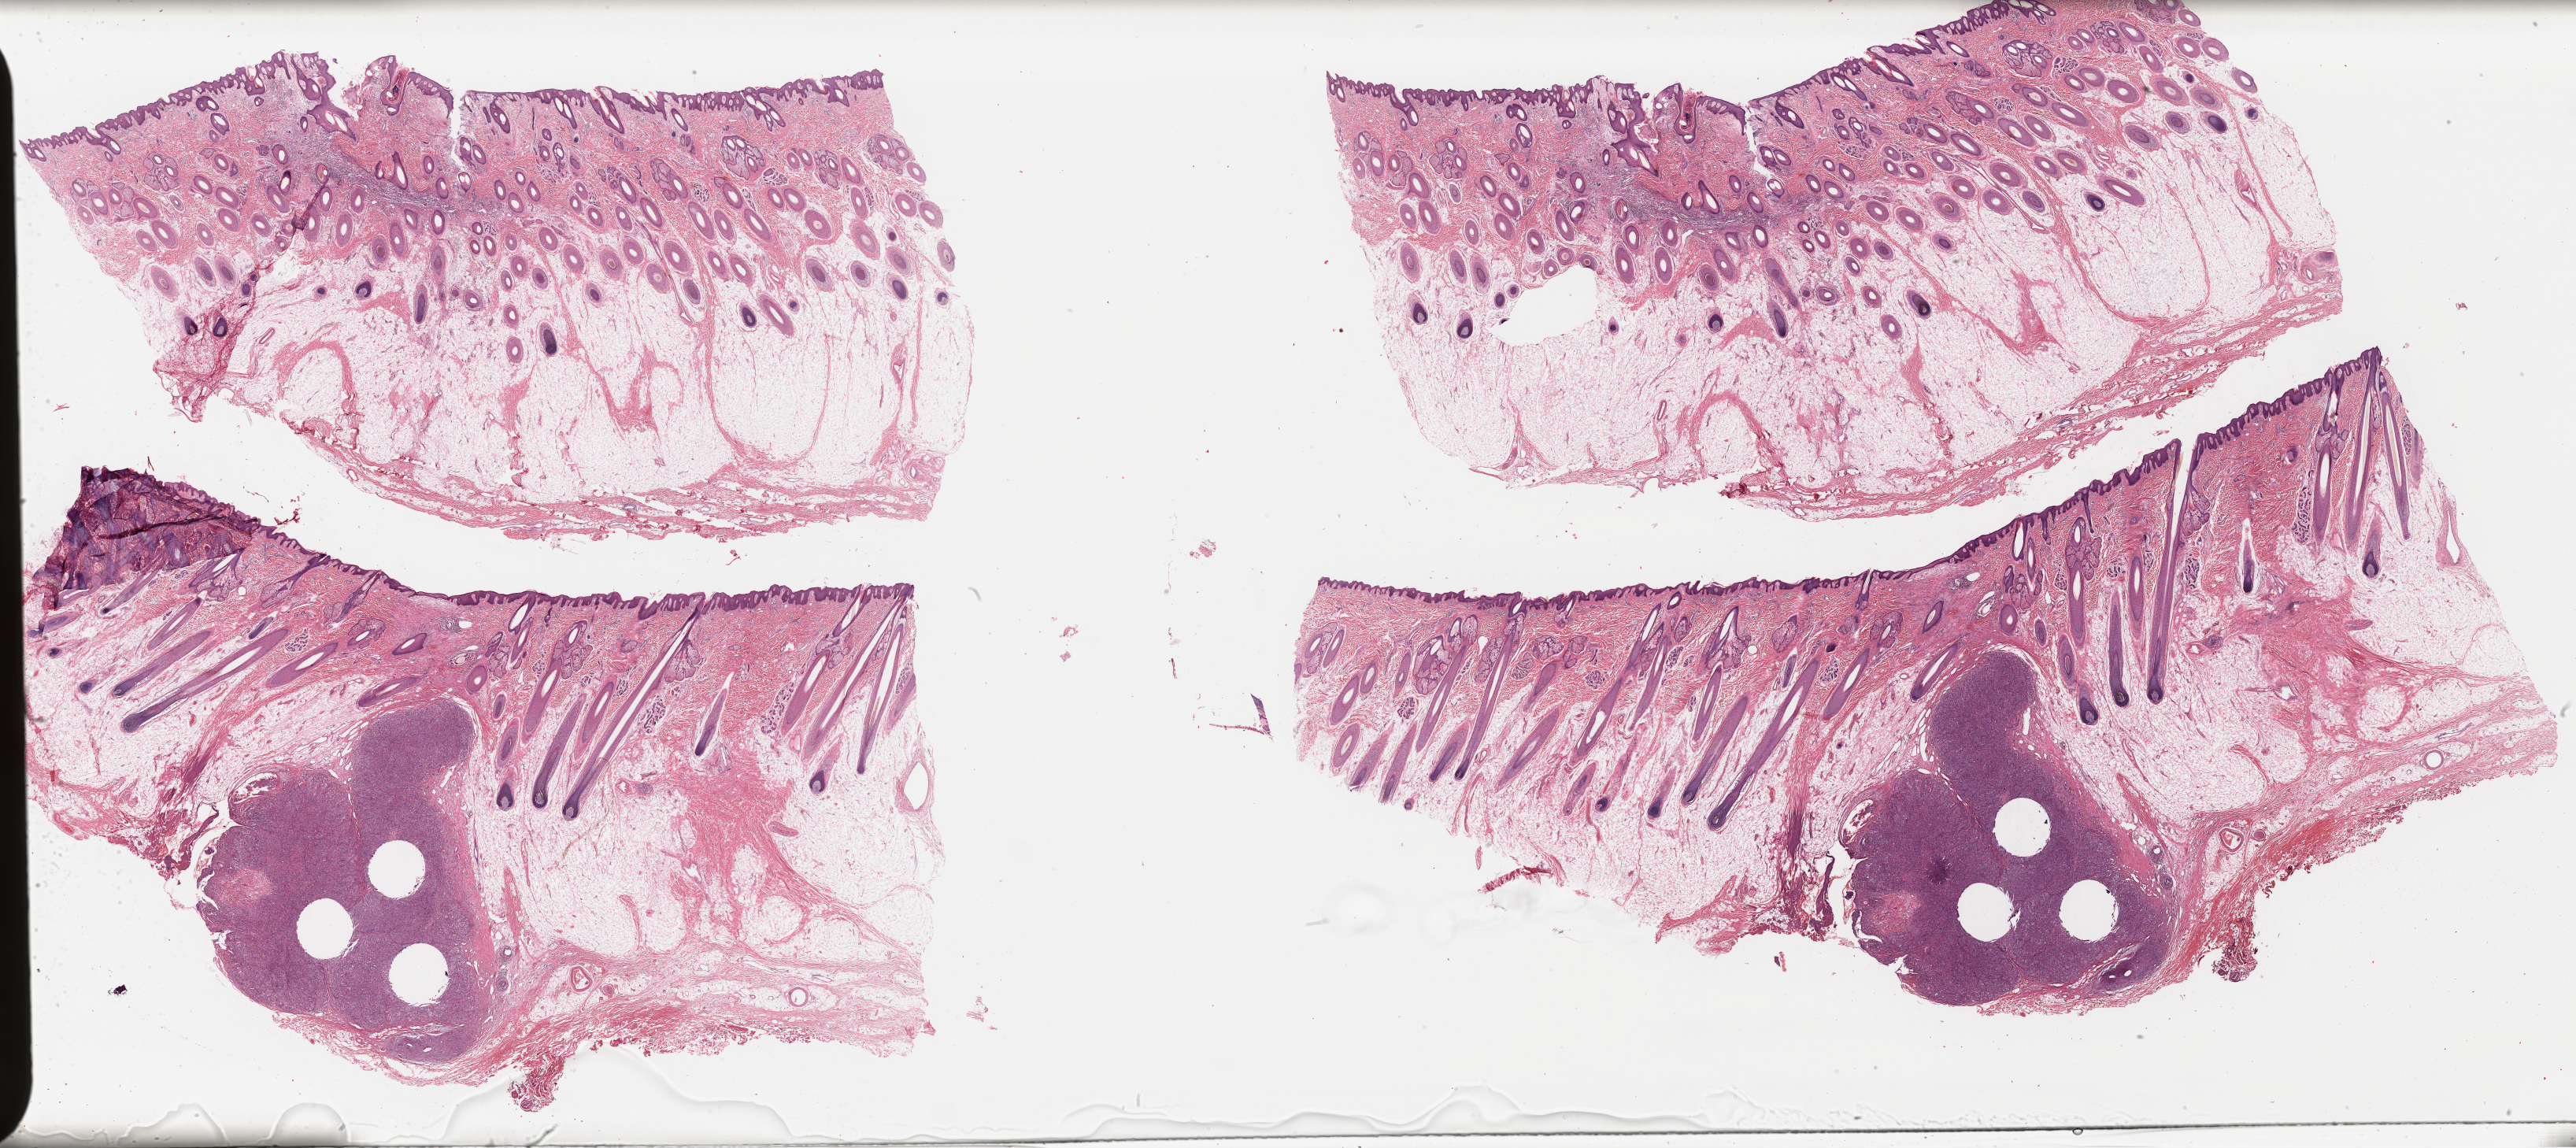
H&E whole-slide image — whole scanned area (about 51.4 x 22.9 mm) shown as a low-resolution overview; FFPE section; metastatic tumour sample, sampled site not recorded. Male patient; age at initial diagnosis 19 years.
This section: metastatic tumour tissue. Patient diagnosis: Malignant melanoma, NOS.